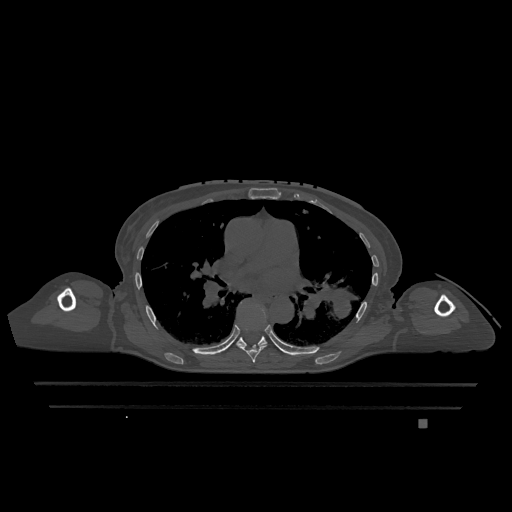
CT including the spine, one axial slice. Slice 766 of 1317 in the series (ordered by position). Bone window (W 1800 / L 400 HU). 512 × 512 image matrix, field of view 500 × 500 mm. Patient: female, 74 years. Case-level facts recorded for this patient, not image findings: primary cancer: lung; vertebrae with lytic lesions (as recorded): T1, T4, T5, T6, L4, L5.
Outlined on this slice (semi-automatically segmented with operator editing):
- T6 vertebra: bounding box (x1, y1, x2, y2) in pixels: (237, 305, 268, 363)
- T7 vertebra: (237, 329, 267, 347)